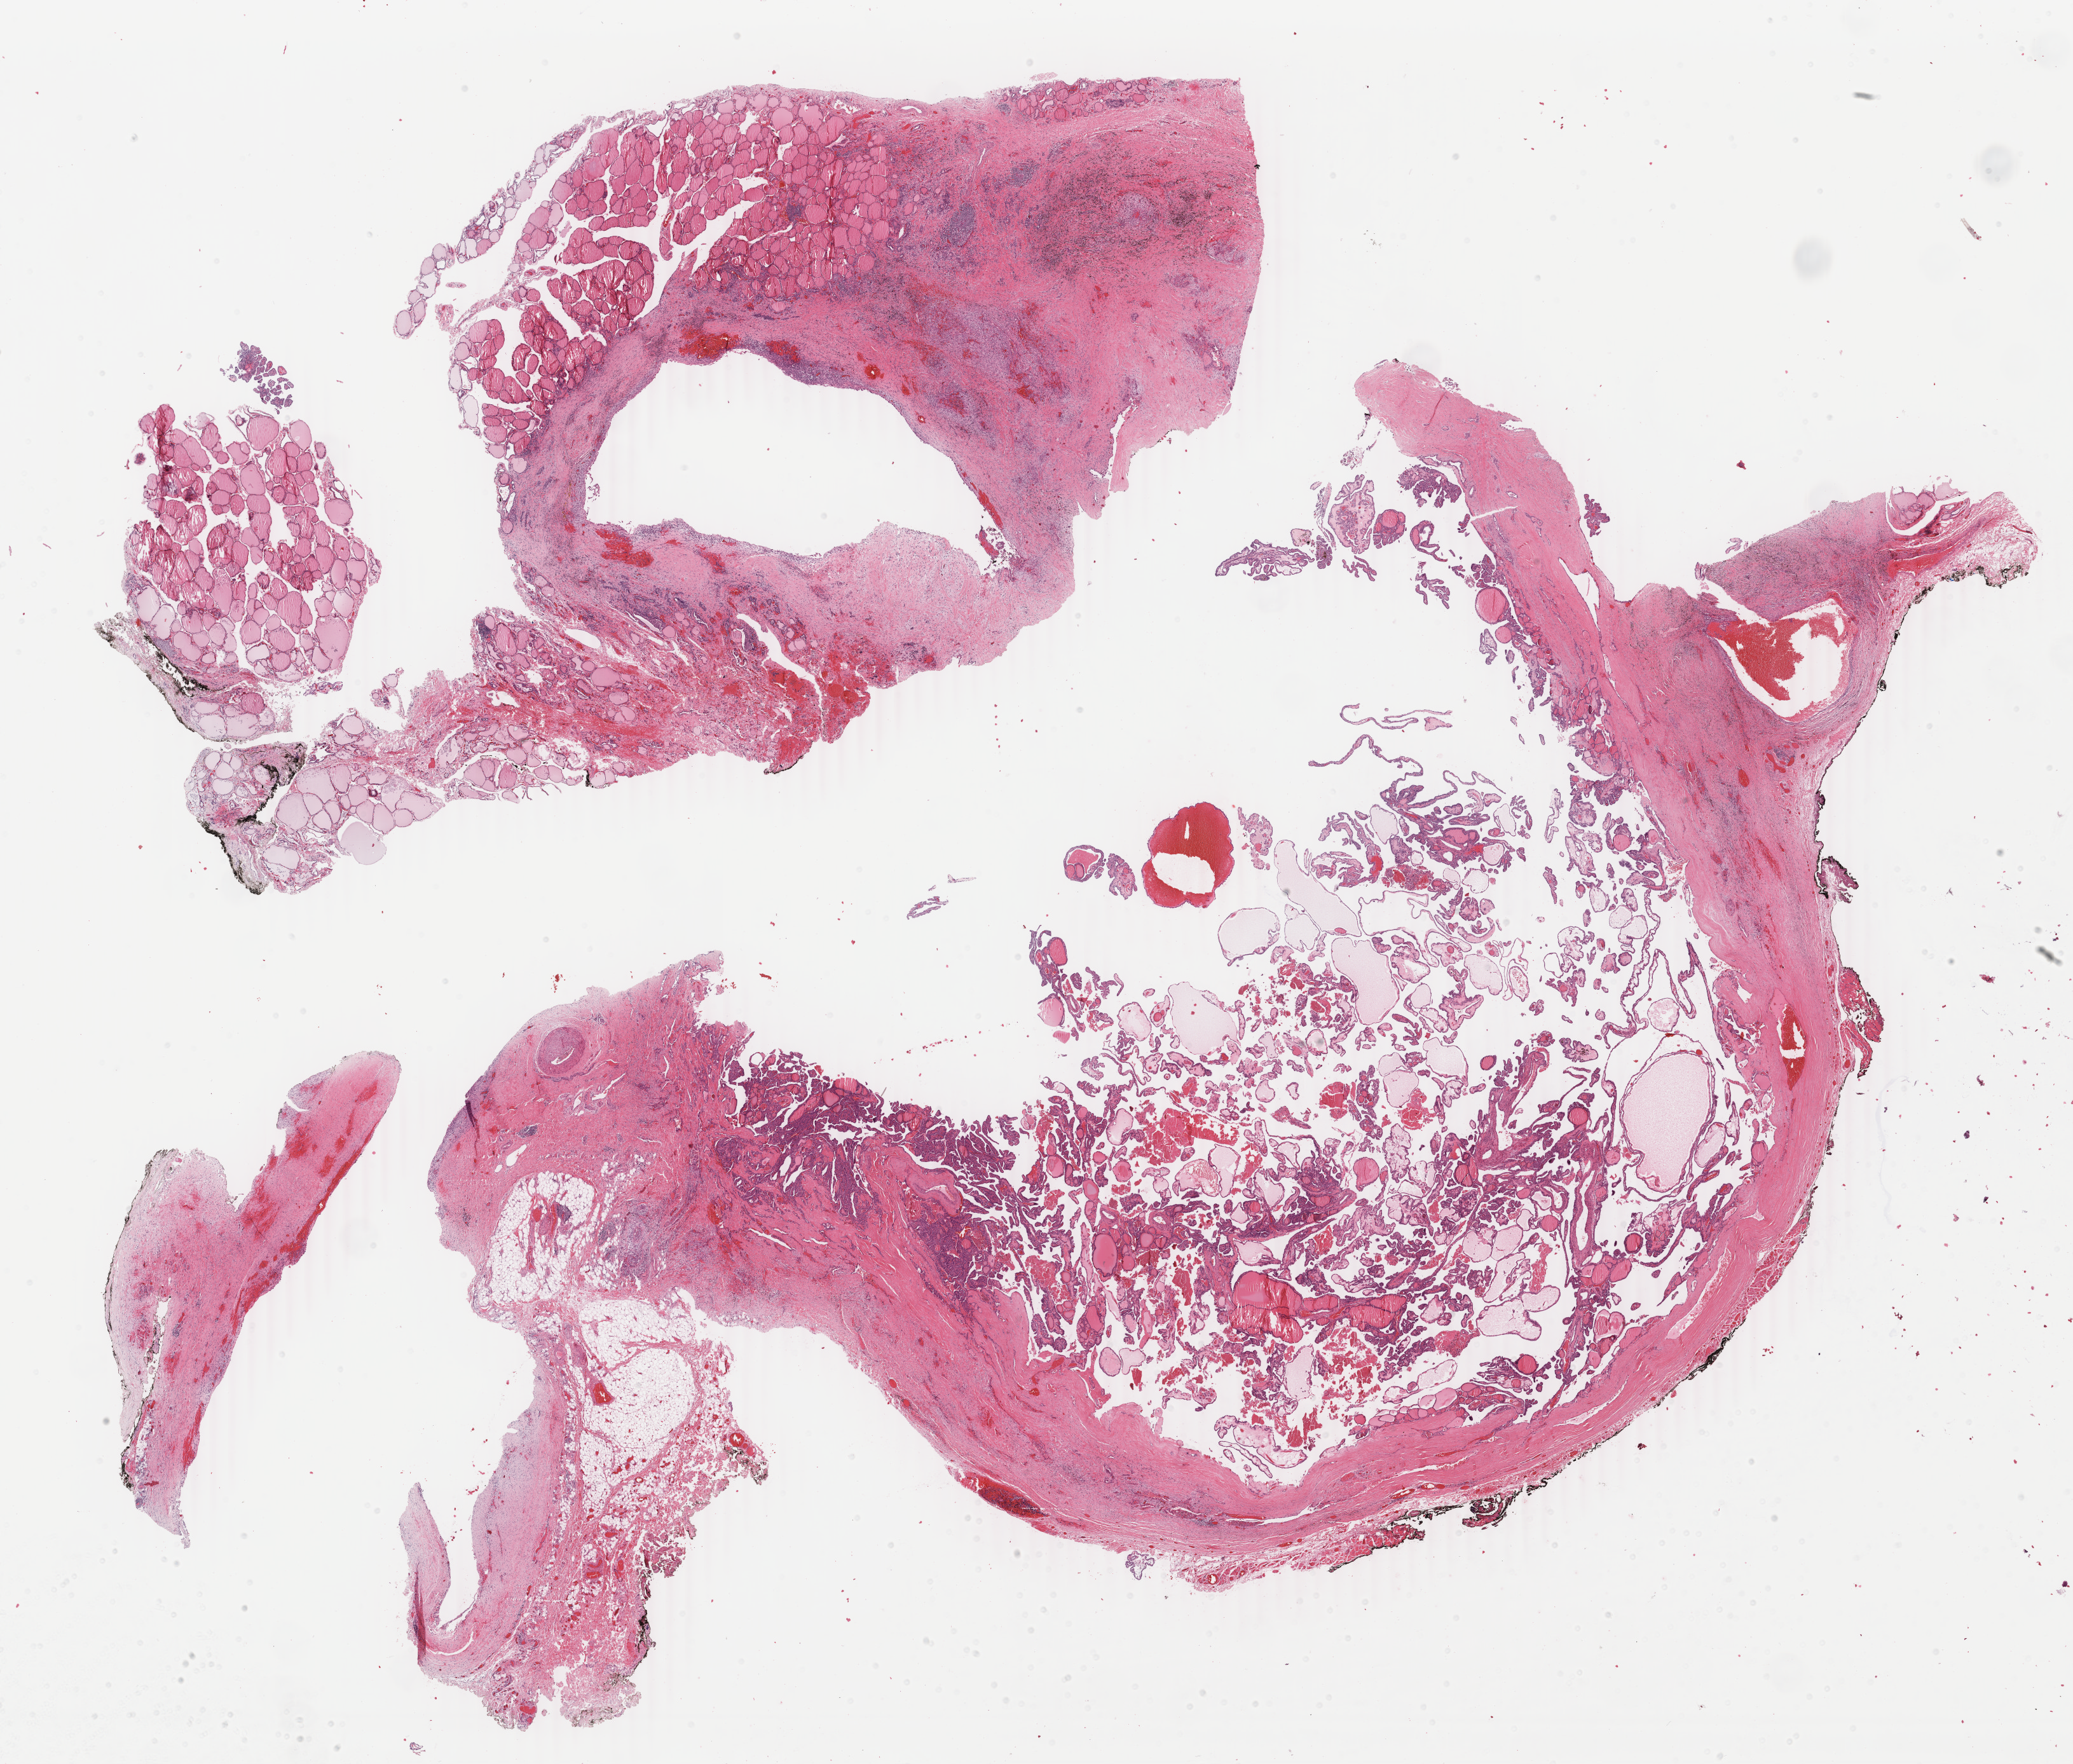
Whole-slide histology image, H&E — low-resolution overview of the scanned area, about 25.9 x 22.1 mm (slide scanned at 40x), FFPE section, sample: primary tumour, thyroid. Patient: male, age at initial diagnosis 33 years.
* pathologic diagnosis: Papillary adenocarcinoma, NOS (thyroid gland)
* lymph nodes positive (case pathology): 5 of 5 examined
* AJCC pathologic stage: I (6th edition)